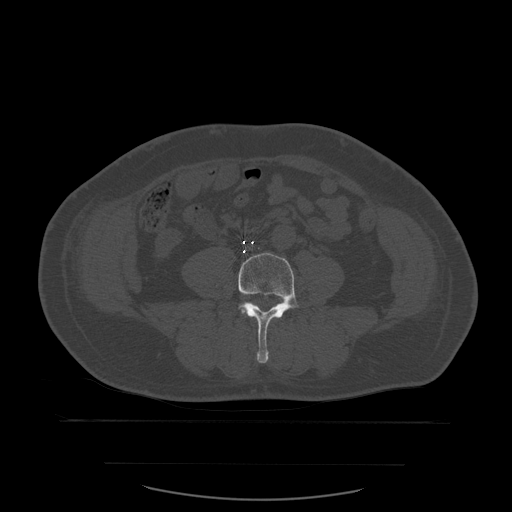
CT including the spine, one axial slice; slice 163 of 590 in the series (ordered by position); bone window (W 1800 / L 400 HU); 1.25 mm slice thickness; 512 × 512 image matrix, field of view 479 × 479 mm. Patient age 71 years. Case-level facts recorded for this patient, not image findings: primary cancer: lung; vertebrae with lytic lesions (as recorded): T1, T2, L5, S1.
Structures marked on this image (semi-automatic segmentation, software-assisted and operator-edited):
- L4 vertebra: bounding box (x1, y1, x2, y2) in pixels: (239, 253, 299, 364)
- L5 vertebra: (250, 302, 254, 305)